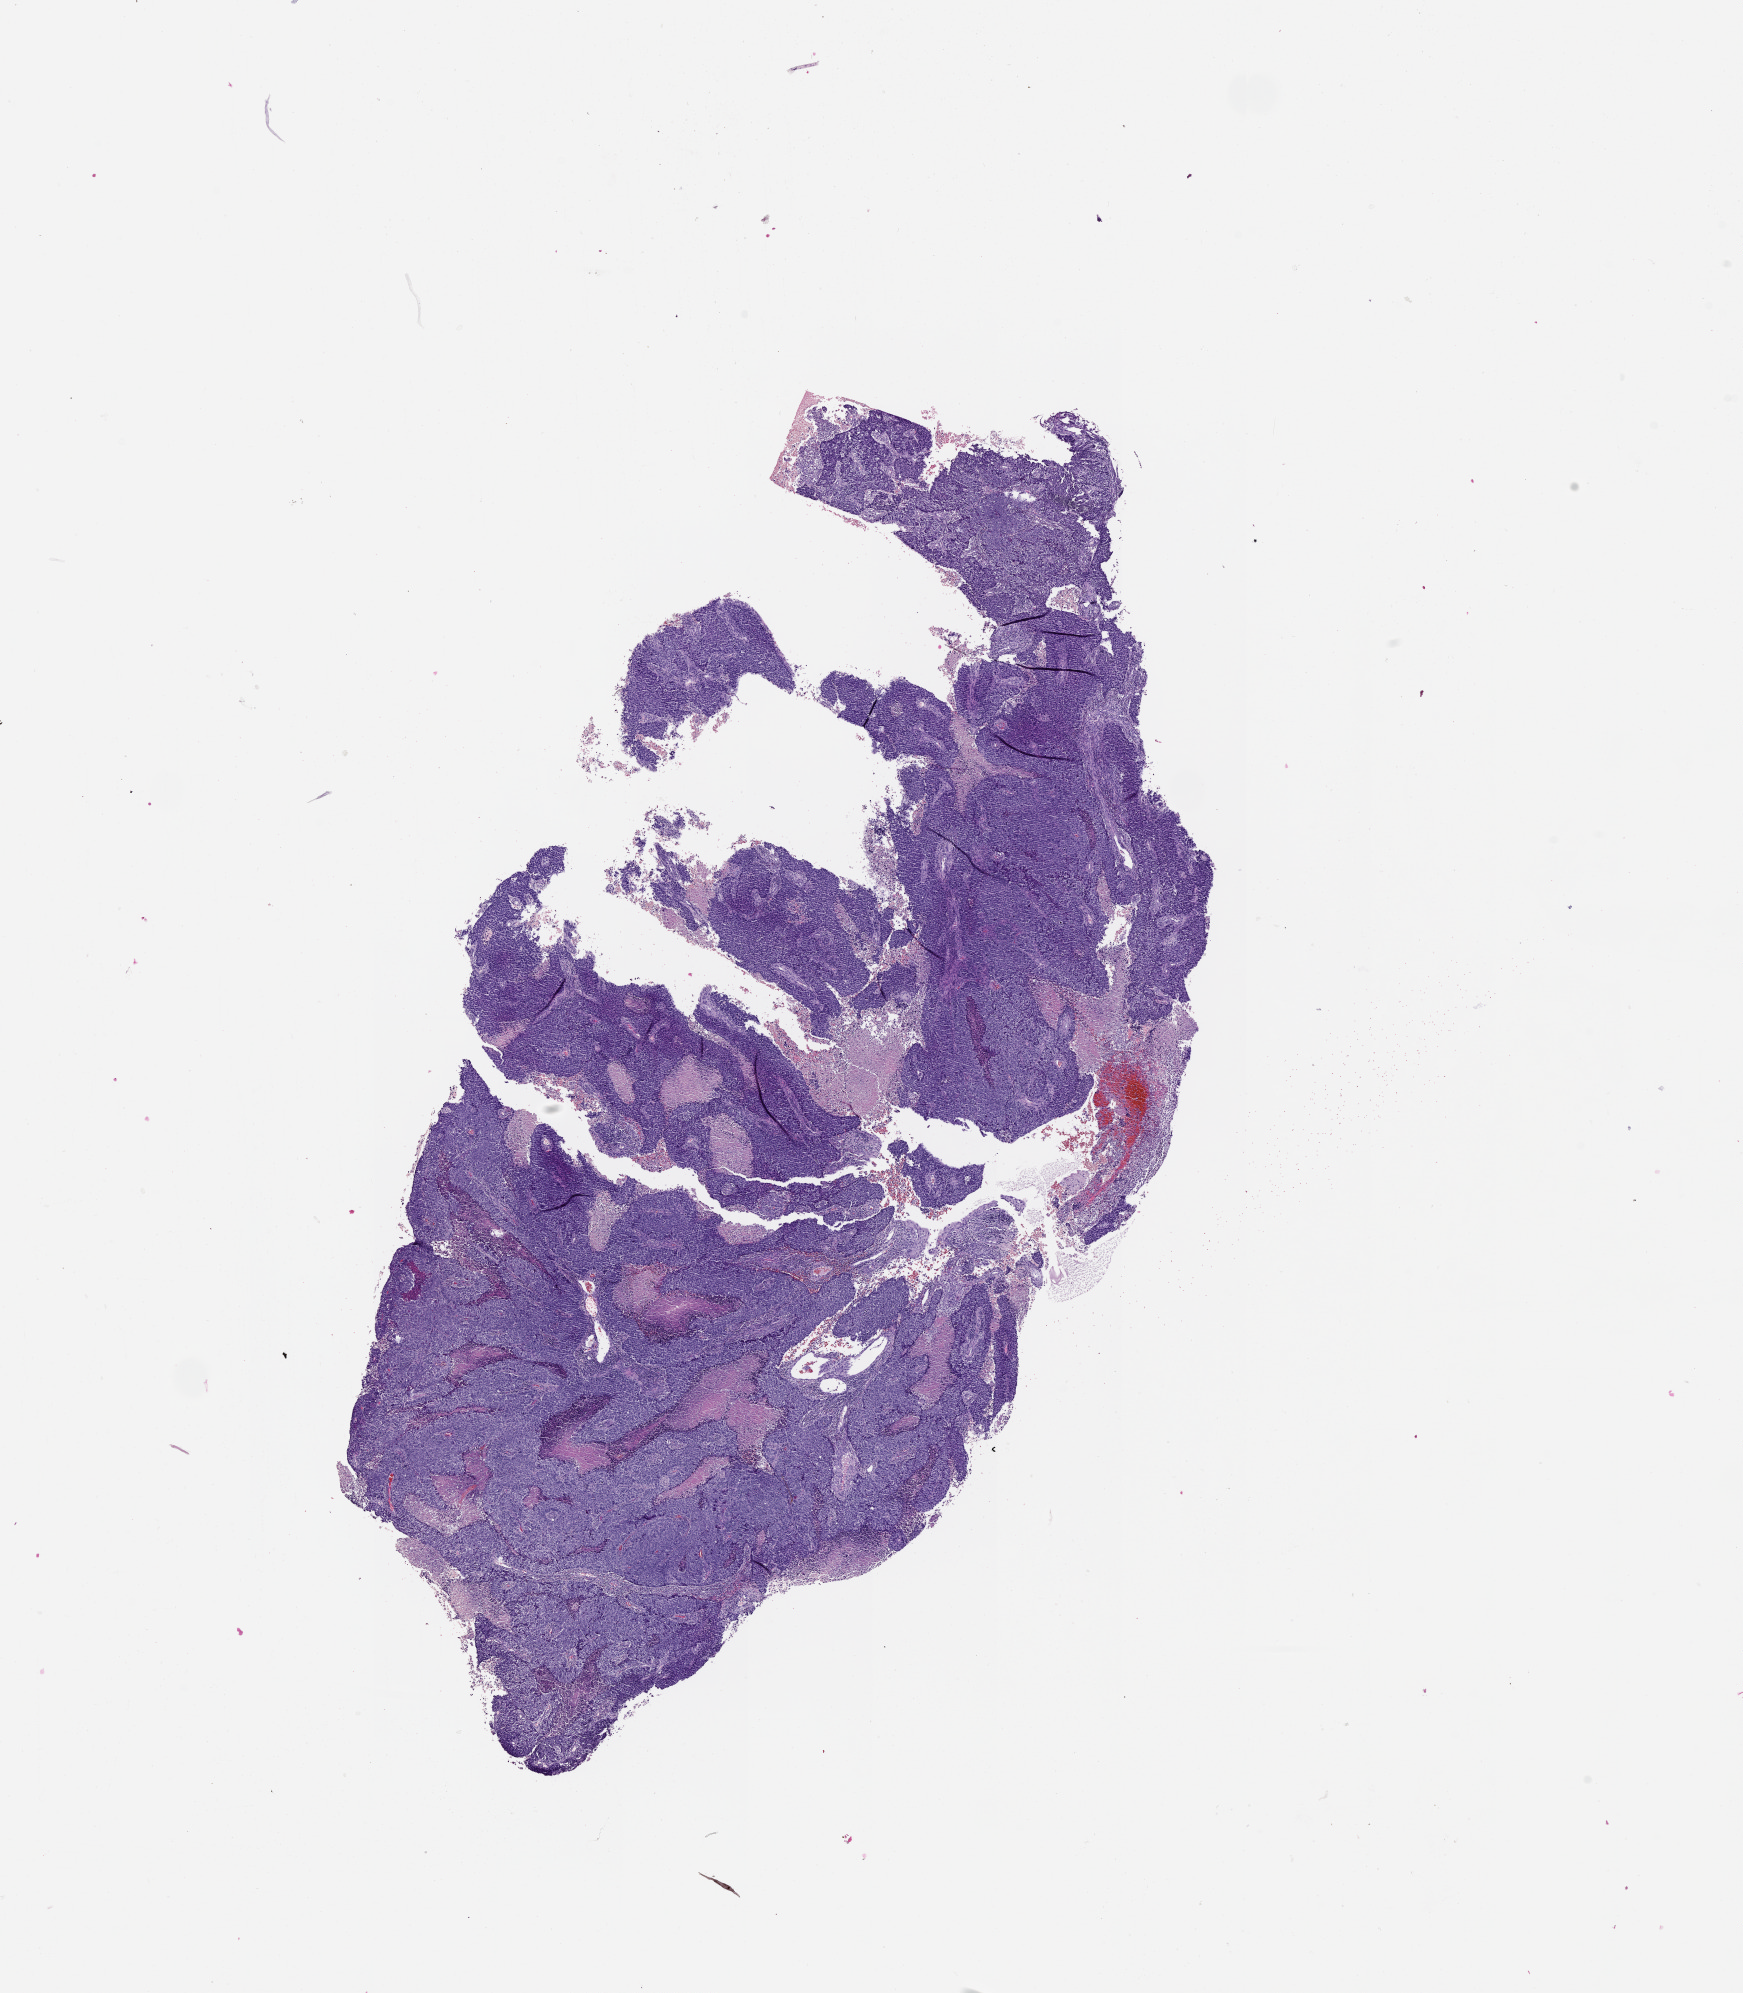
Whole-slide histology image, H&E-stained, shown as a low-resolution overview of the whole scanned area (about 14.0 x 16.0 mm, slide scanned at 20x). Lung, tumour tissue. 60-year-old male patient.
Patient diagnosis (cohort enrolment): squamous cell carcinoma (lung).